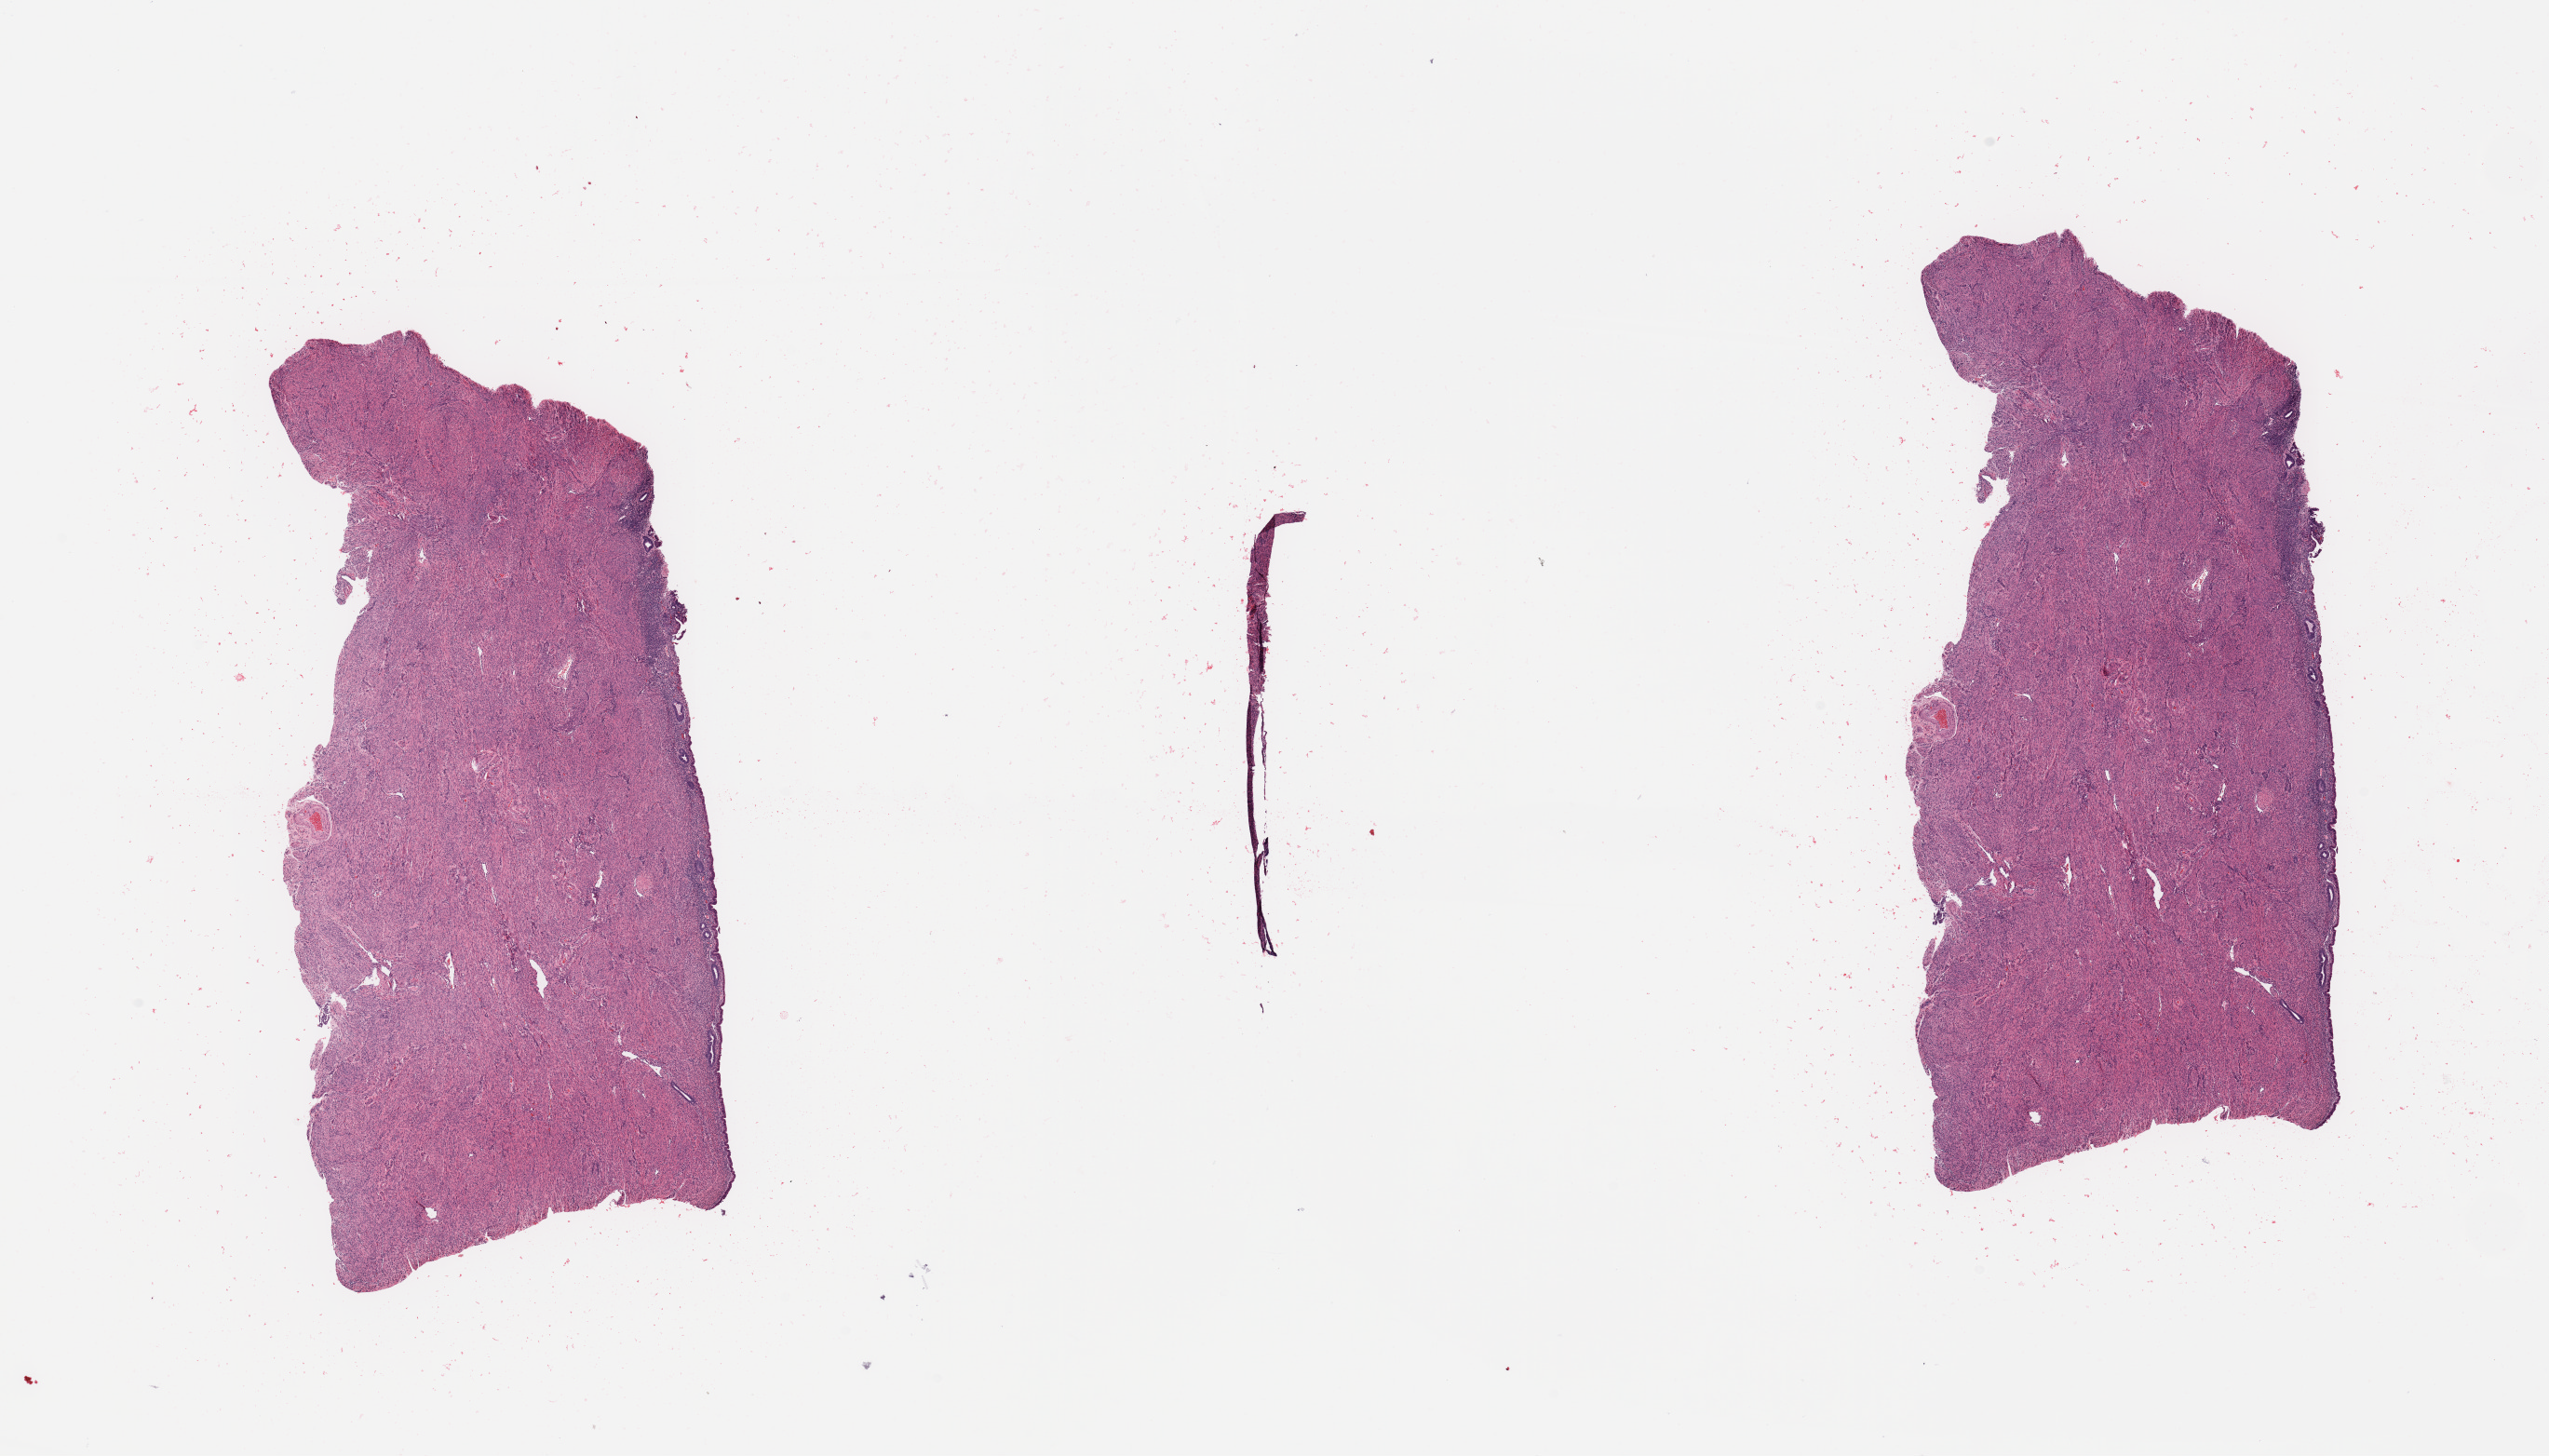
Digitized H&E tissue section (whole slide) — low-resolution overview of the scanned area, about 21.7 x 12.4 mm (slide scanned at 20x), normal (non-tumour) tissue sample, sampled site: uterus. Female, 64 y/o.
This section: normal (non-tumour) tissue from the same patient. Patient diagnosis: Endometrioid adenocarcinoma, NOS.